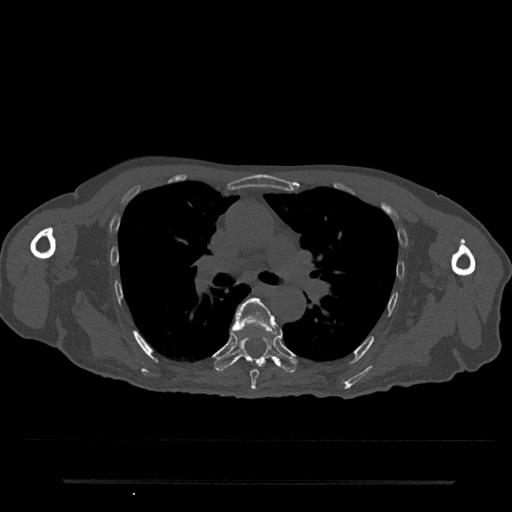
CT including the spine, one axial slice; position 504 of 797 along the scan axis; reconstruction kernel Br40s/3; bone window (W 1800 / L 400 HU); 0.5 mm slice thickness; 512 × 512 image matrix, field of view 427 × 427 mm. Patient: male, 74 years. Case-level facts recorded for this patient, not image findings: primary cancer: prostate.
Annotated regions visible in this slice (semi-automatically segmented with operator editing):
- T6 vertebra: bounding box [x1, y1, x2, y2] px = [231, 298, 279, 390]
- T7 vertebra: [215, 338, 297, 372]